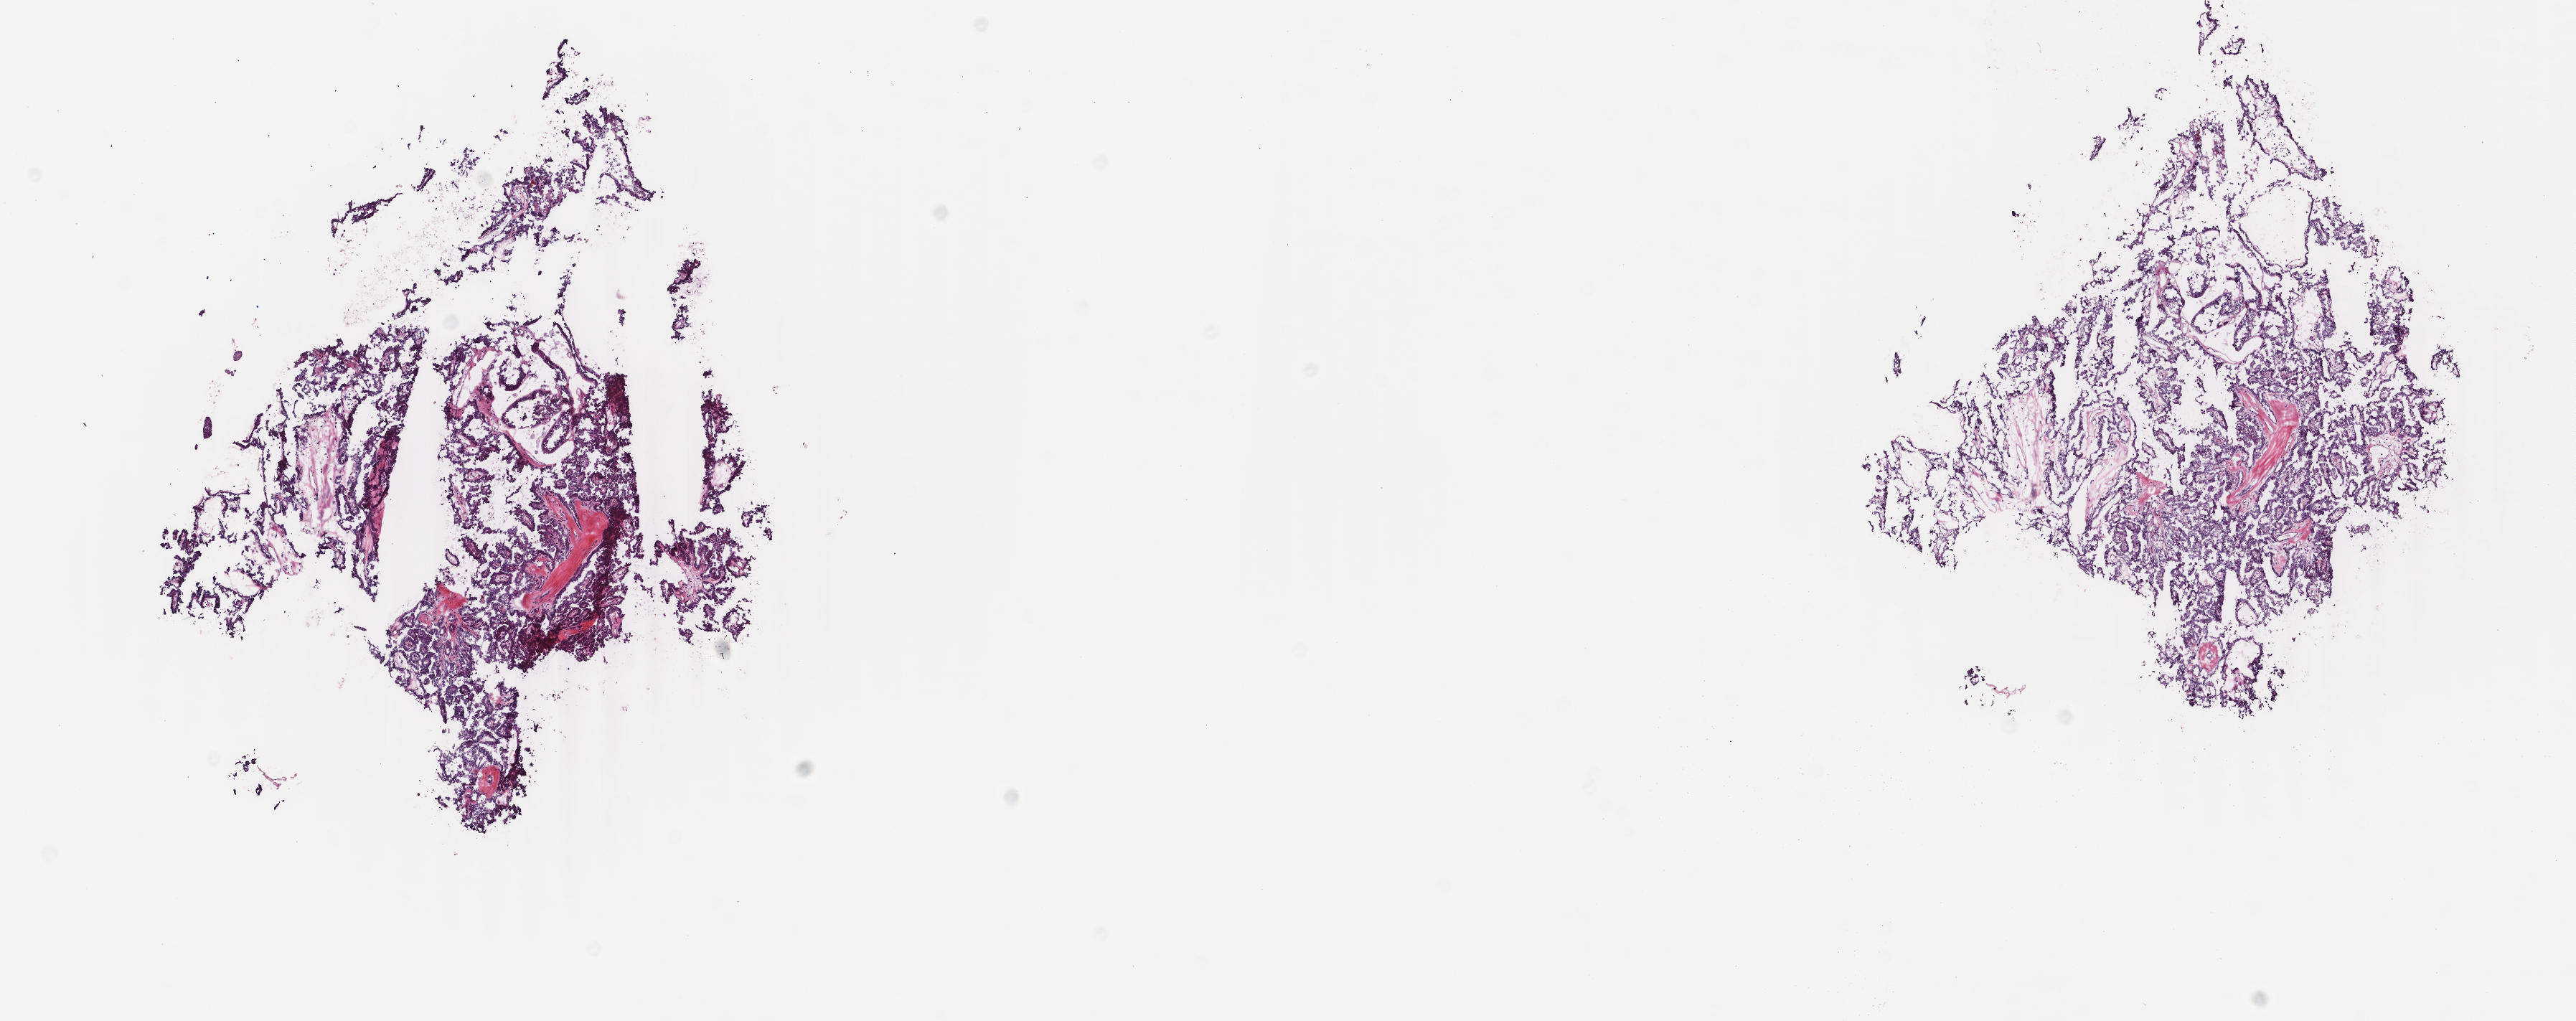
Digitized H&E tissue section (whole slide), low-resolution overview of the scanned area, about 14.3 x 5.7 mm (slide scanned at 40x), frozen section from the bottom of the tissue portion, primary tumour sample from the thyroid. Female patient; age at initial diagnosis 30 years. Pathologist review of this section (percent, as recorded): tumour cells 95%, tumour nuclei 95%, normal cells 0%, stromal cells 5%, necrosis 0%. Inflammatory infiltration, as recorded: lymphocyte infiltration 0%, monocyte infiltration 0%, neutrophil infiltration 0%.
AJCC pathologic stage: I (7th edition). Pathologic diagnosis: Papillary adenocarcinoma, NOS (thyroid gland).